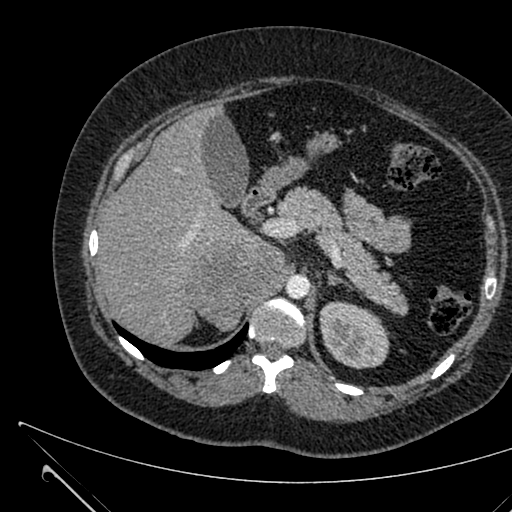
Contrast-enhanced abdominal CT, one axial slice; slice 436 of 731 in the series (ordered by position); 120 kVp; soft-tissue window (W 400 / L 40 HU); 512 × 512 image matrix, field of view 376 × 376 mm. Patient: female, 36 years. From the clinical record (not read from this slice): diagnosis: adrenocortical carcinoma; tumour side: right adrenal; tumour size at pathology: 10 cm; Ki-67 index: 20 %; stage (as recorded): 4.
Annotated regions visible in this slice (semi-automatically segmented with operator editing):
- mass: bounding box (x1, y1, x2, y2) in pixels: (188, 243, 285, 329)